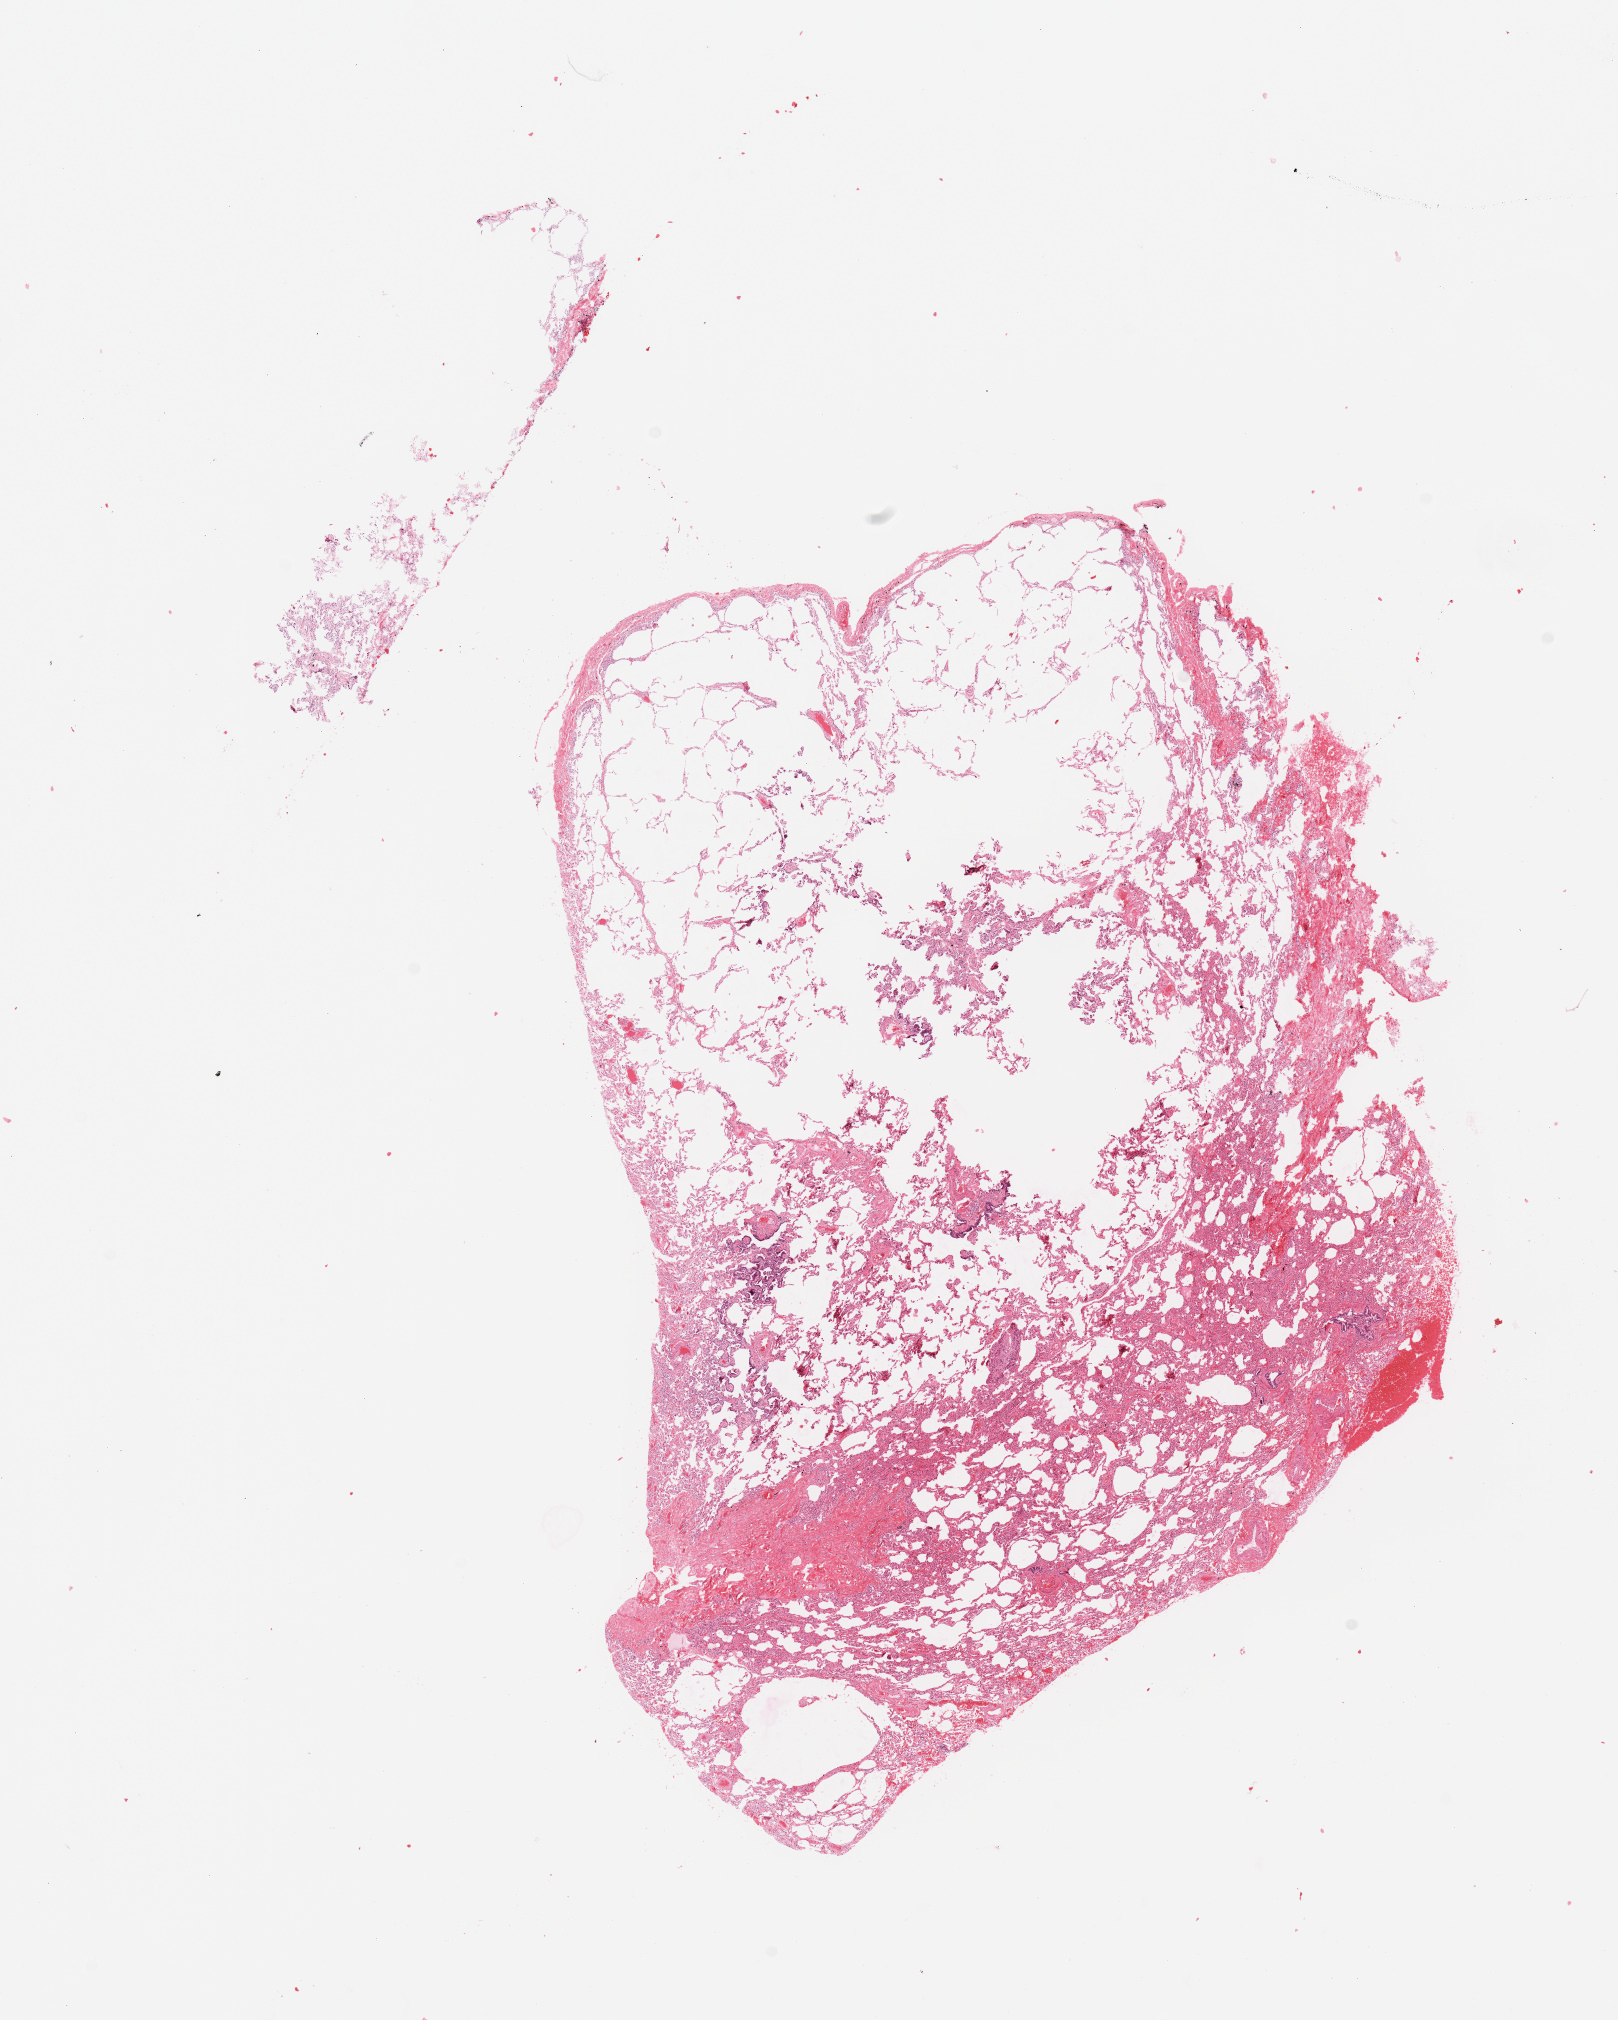
H&E-stained whole-slide image — whole scanned area (about 12.8 x 16.0 mm, acquisition: 20x scan) shown as a low-resolution overview, normal (non-tumour) tissue sample, sampled site: lung. 43-year-old female patient.
- this section: normal (non-tumour) tissue from the same patient
- patient diagnosis: Adenocarcinoma, NOS